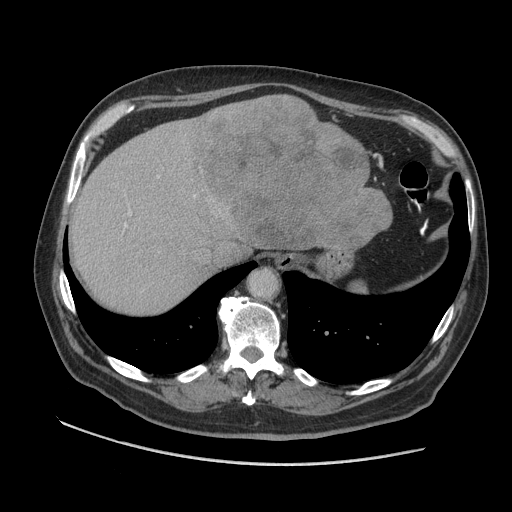
Contrast-enhanced abdominal CT (liver protocol), one axial slice; slice 77 of 109 in the series (ordered by position); reconstruction kernel STANDARD; 140 kVp; soft-tissue window (W 400 / L 40 HU); 2.5 mm slice thickness; 512 × 512 image matrix, field of view 420 × 420 mm. From the clinical record (not read from this slice): diagnosis: hepatocellular carcinoma (patient treated with transarterial chemoembolisation; whether this scan precedes or follows treatment is not stated here); TNM stage (as recorded): Stage-I; Child-Pugh class: A; tumour nodularity: uninodular.
Structures marked on this image (semi-automatically segmented with operator editing):
- abdominal aorta: box from (x=250, y=270) to (x=276, y=297) px
- liver parenchyma outside the tumour (the mass and vessels are separate outlines, so this box may not span the whole liver): (x=70, y=102)–(x=332, y=314)
- mass: (x=192, y=94)–(x=393, y=257)
- liver vessels: (x=125, y=176)–(x=196, y=228)